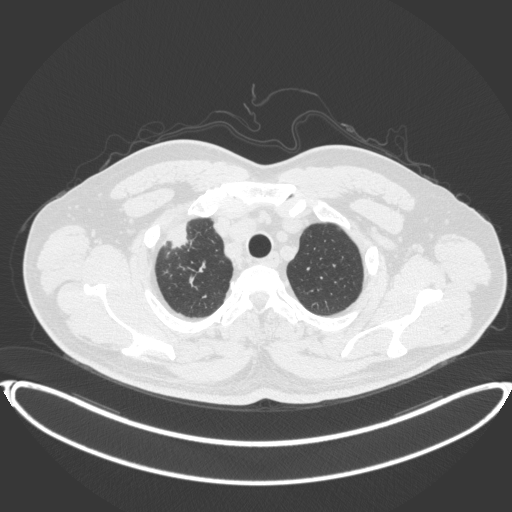
Chest CT, one axial slice. 120 kVp. Lung window (W 1500 / L -600 HU). 1 mm slice thickness. 512 × 512 image matrix. Male patient, age 53 years. Case-level facts recorded for this patient, not image findings: clinical TNM (as recorded): T2a N0 M0.
Annotated regions visible in this slice (bounding box drawn by a radiologist):
- lung tumour (recorded histology: adenocarcinoma): bounding box [x1, y1, x2, y2] px = [166, 219, 198, 251]